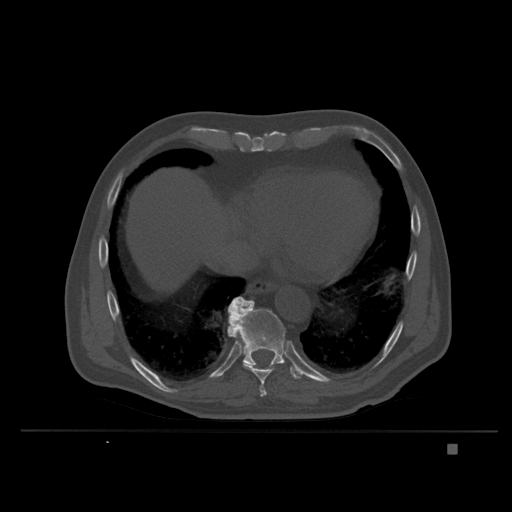
CT including the spine, one axial slice; slice 204 of 435 in the series (ordered by position); bone window (W 1800 / L 400 HU); 1.5 mm slice thickness; 512 × 512 image matrix, field of view 434 × 434 mm. Patient: male, 73 years. Case-level facts recorded for this patient, not image findings: primary cancer: skin.
Annotated regions visible in this slice (semi-automatically segmented with operator editing):
- T10 vertebra: bounding box [x1, y1, x2, y2] px = [229, 300, 301, 379]
- T9 vertebra: [227, 296, 285, 397]